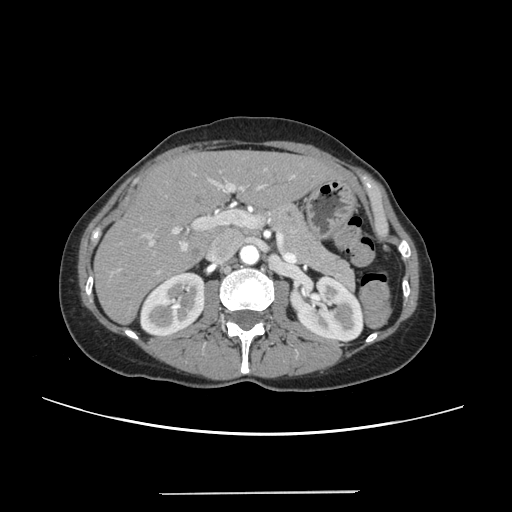
Contrast-enhanced abdominal CT, one axial slice; slice 136 of 240 in the series (ordered by position); intravenous contrast given; soft-tissue window (W 400 / L 40 HU); 512 × 512 image matrix, field of view 371 × 371 mm. Female patient, age 60 years. Case-level facts recorded for this patient, not image findings: diagnosis: colorectal cancer liver metastases, imaged before liver resection; multiple liver metastases: no; largest metastasis: 1.5 cm.
Structures marked on this image (manually delineated by an expert):
- liver: bounding box [x1, y1, x2, y2] px = [95, 152, 338, 323]
- planned liver remnant (the part of the liver to remain after resection): [95, 152, 338, 323]
- portal vein (with intrahepatic branches): [112, 169, 295, 274]